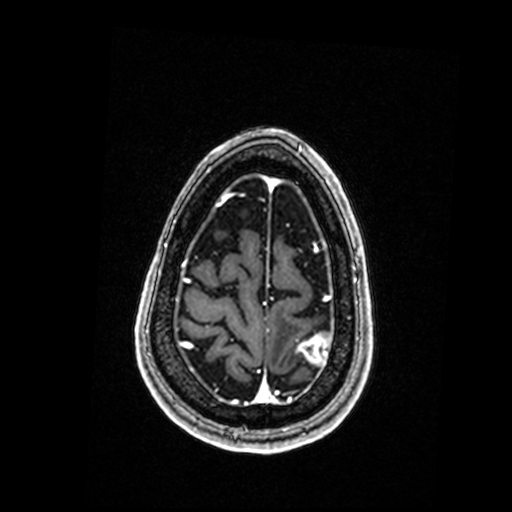
Brain MRI from a brain-tumour surgery series, one axial slice. Position 39 of 192 along the scan axis. T1-weighted post-contrast. 512 × 512 image matrix, field of view 250 × 250 mm. From the clinical record (not read from this slice): histopathology: Metastastic Carcinoma, Poorly Differentiated; tumour location: Left Parietal.
Annotated regions visible in this slice (outlined manually by an expert reader):
- tumour: box from (x=298, y=334) to (x=332, y=365) px